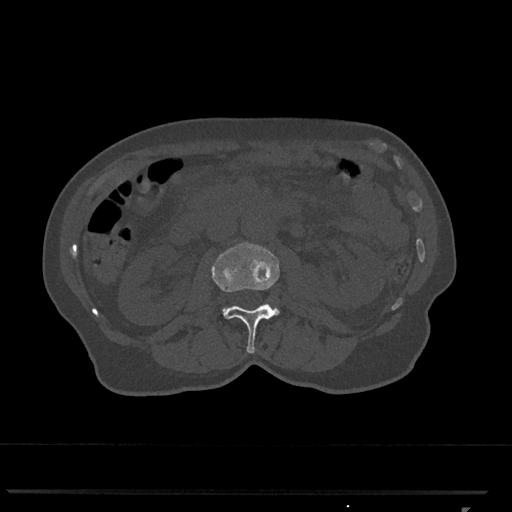
CT including the spine, one axial slice. Reconstruction kernel Br40s/3. 120 kVp. Bone window (W 1800 / L 400 HU). 0.5 mm slice thickness. 512 × 512 image matrix, field of view 380 × 380 mm. Patient: female, 62 years. From the clinical record (not read from this slice): primary cancer: renal.
Structures marked on this image (semi-automatic segmentation, software-assisted and operator-edited):
- L2 vertebra: bounding box [x1, y1, x2, y2] px = [212, 242, 280, 353]